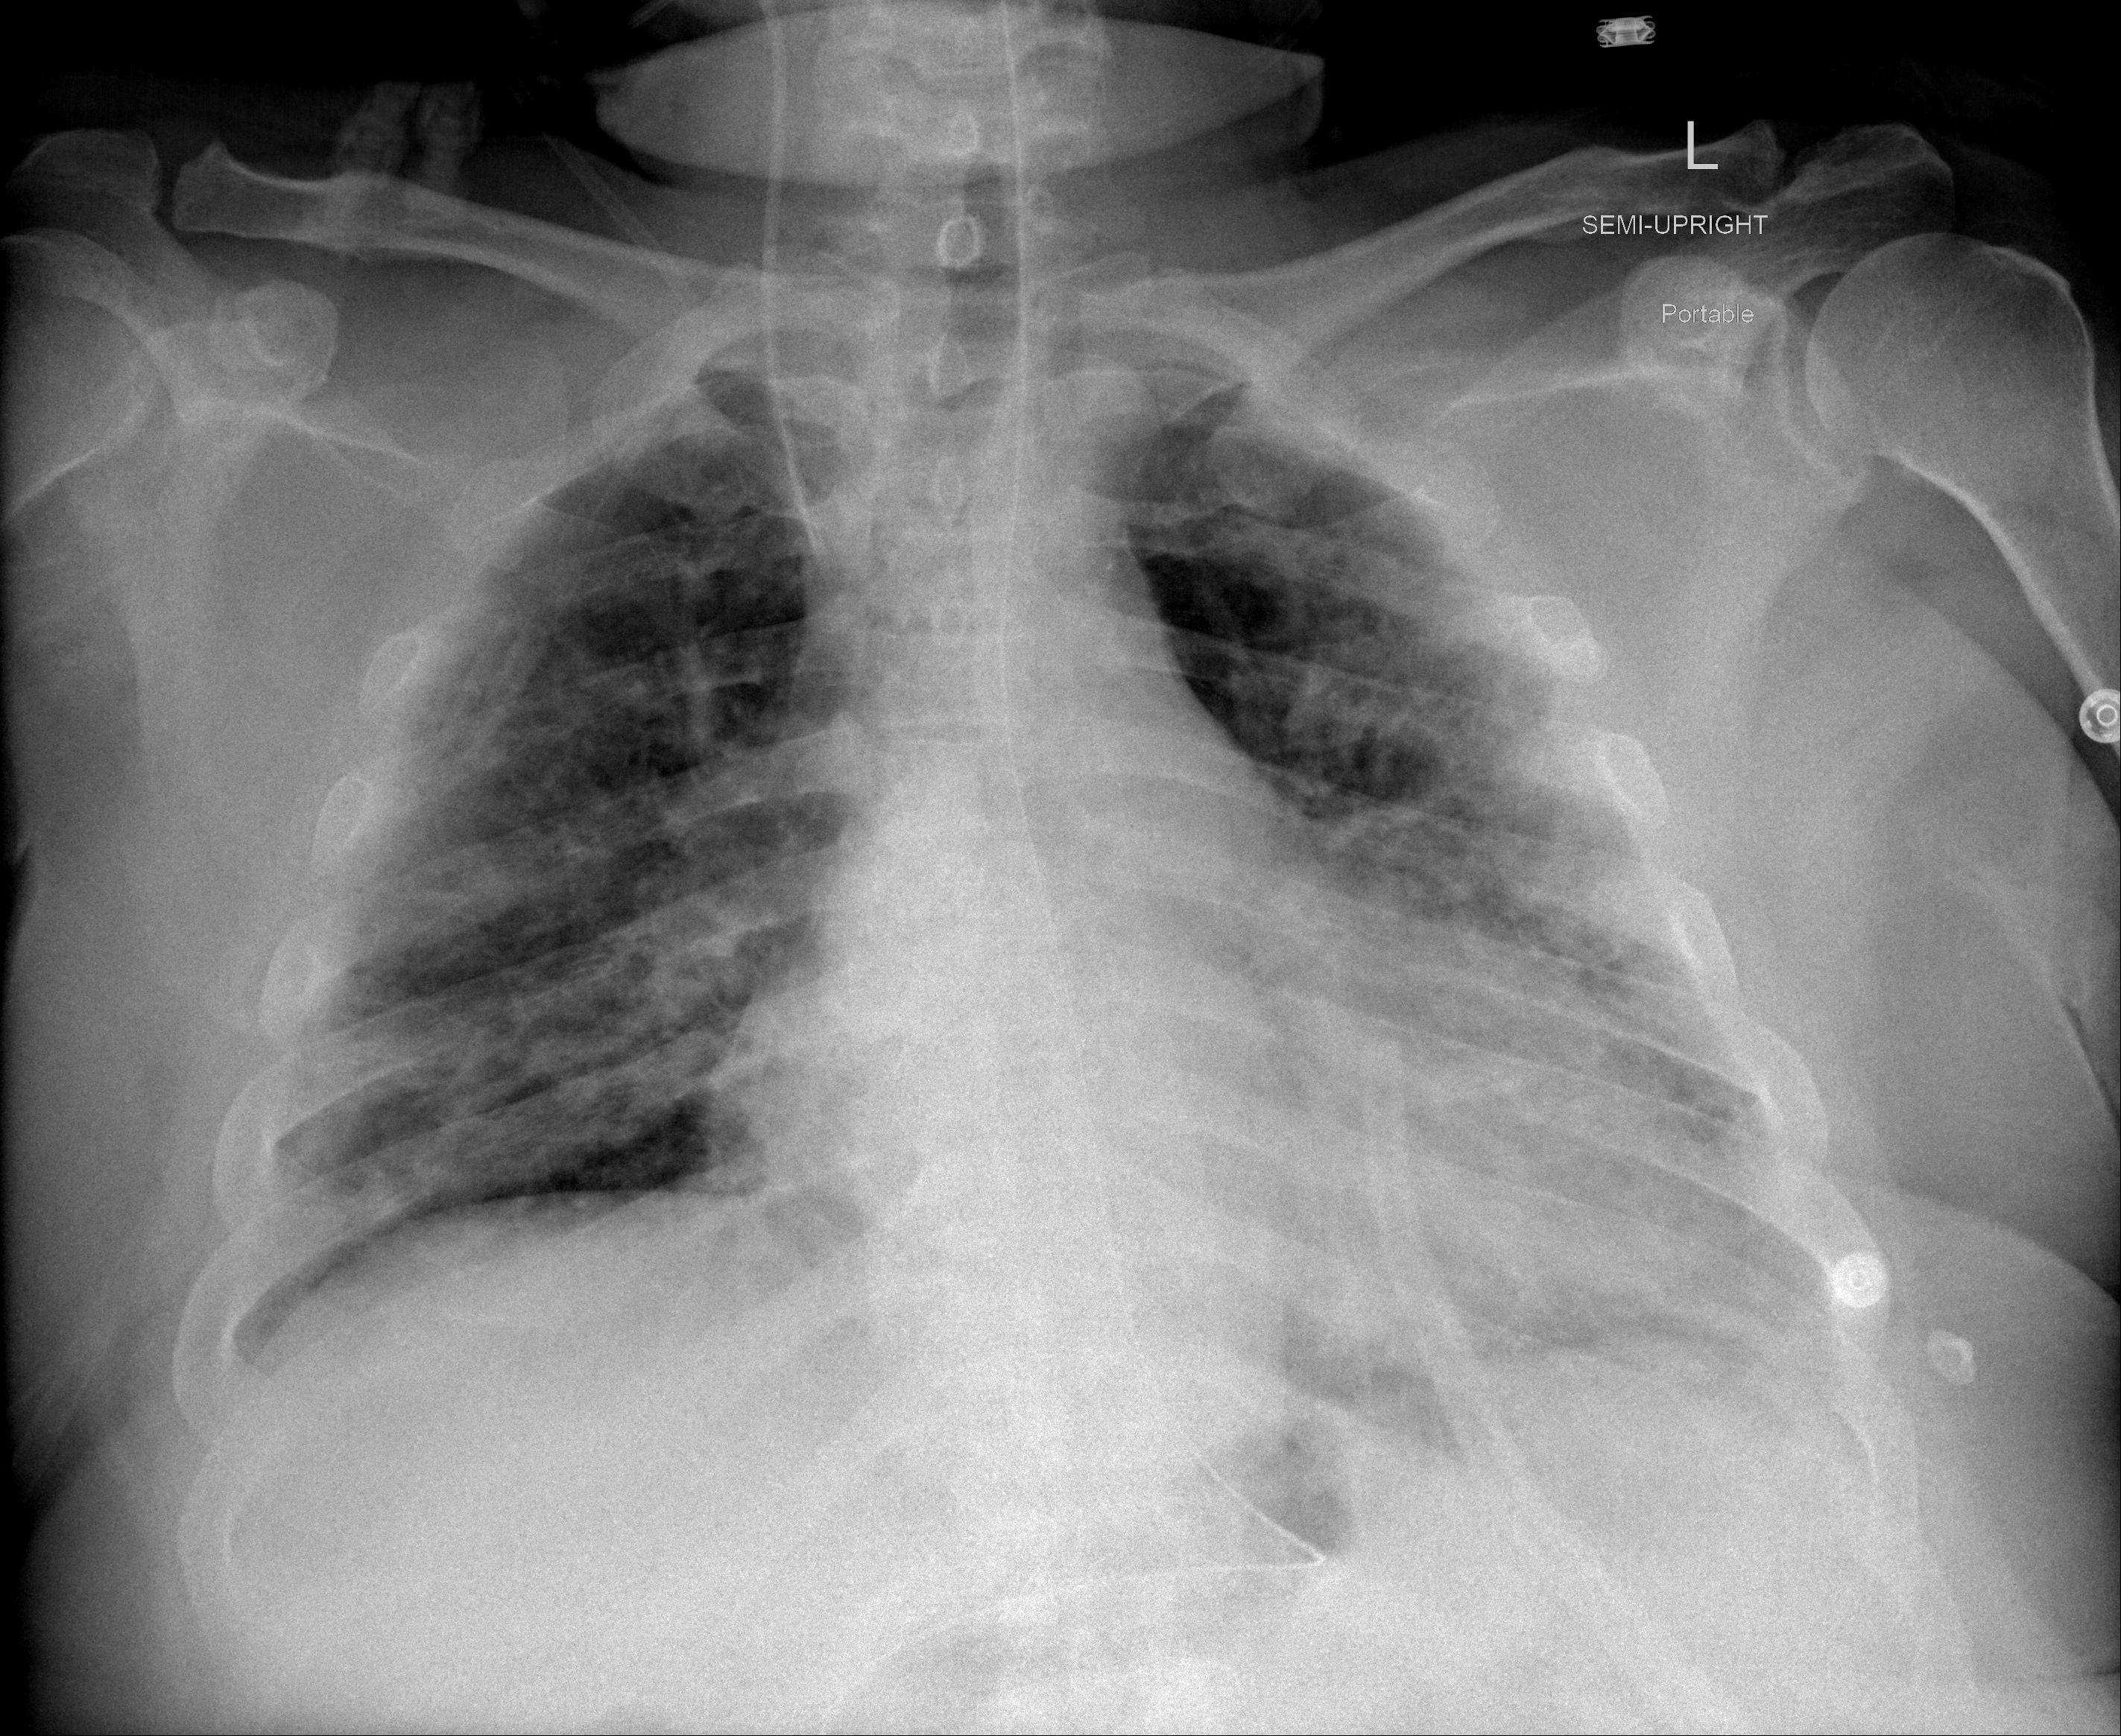
Chest X-ray (portable), AP projection. Male patient, age 55 years; imaged 17 days after the COVID-19 diagnosis.
Radiologist key findings (as recorded): Bibasilar consolidation and/or atelectasis with small left pleural effusion, increased from the previous exam.